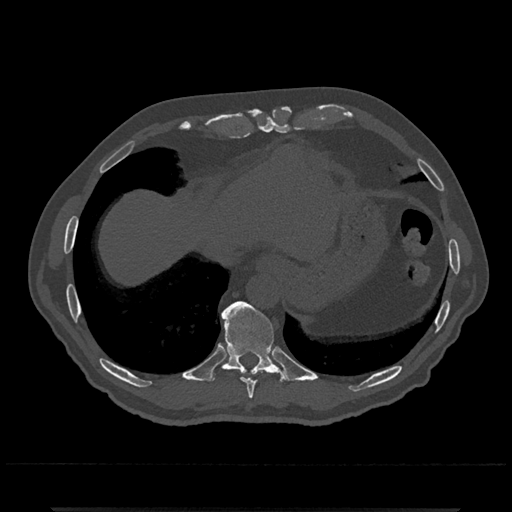
CT including the spine, one axial slice. Position 577 of 797 along the scan axis. Reconstruction kernel Br40s/3. 120 kVp. Bone window (W 1800 / L 400 HU). 512 × 512 image matrix. Patient: male, 67 years. Case-level facts recorded for this patient, not image findings: primary cancer: prostate.
Outlined on this slice (semi-automatically segmented with operator editing):
- T10 vertebra: bounding box (x1, y1, x2, y2) in pixels: (211, 301, 289, 385)
- T9 vertebra: (242, 378, 256, 399)